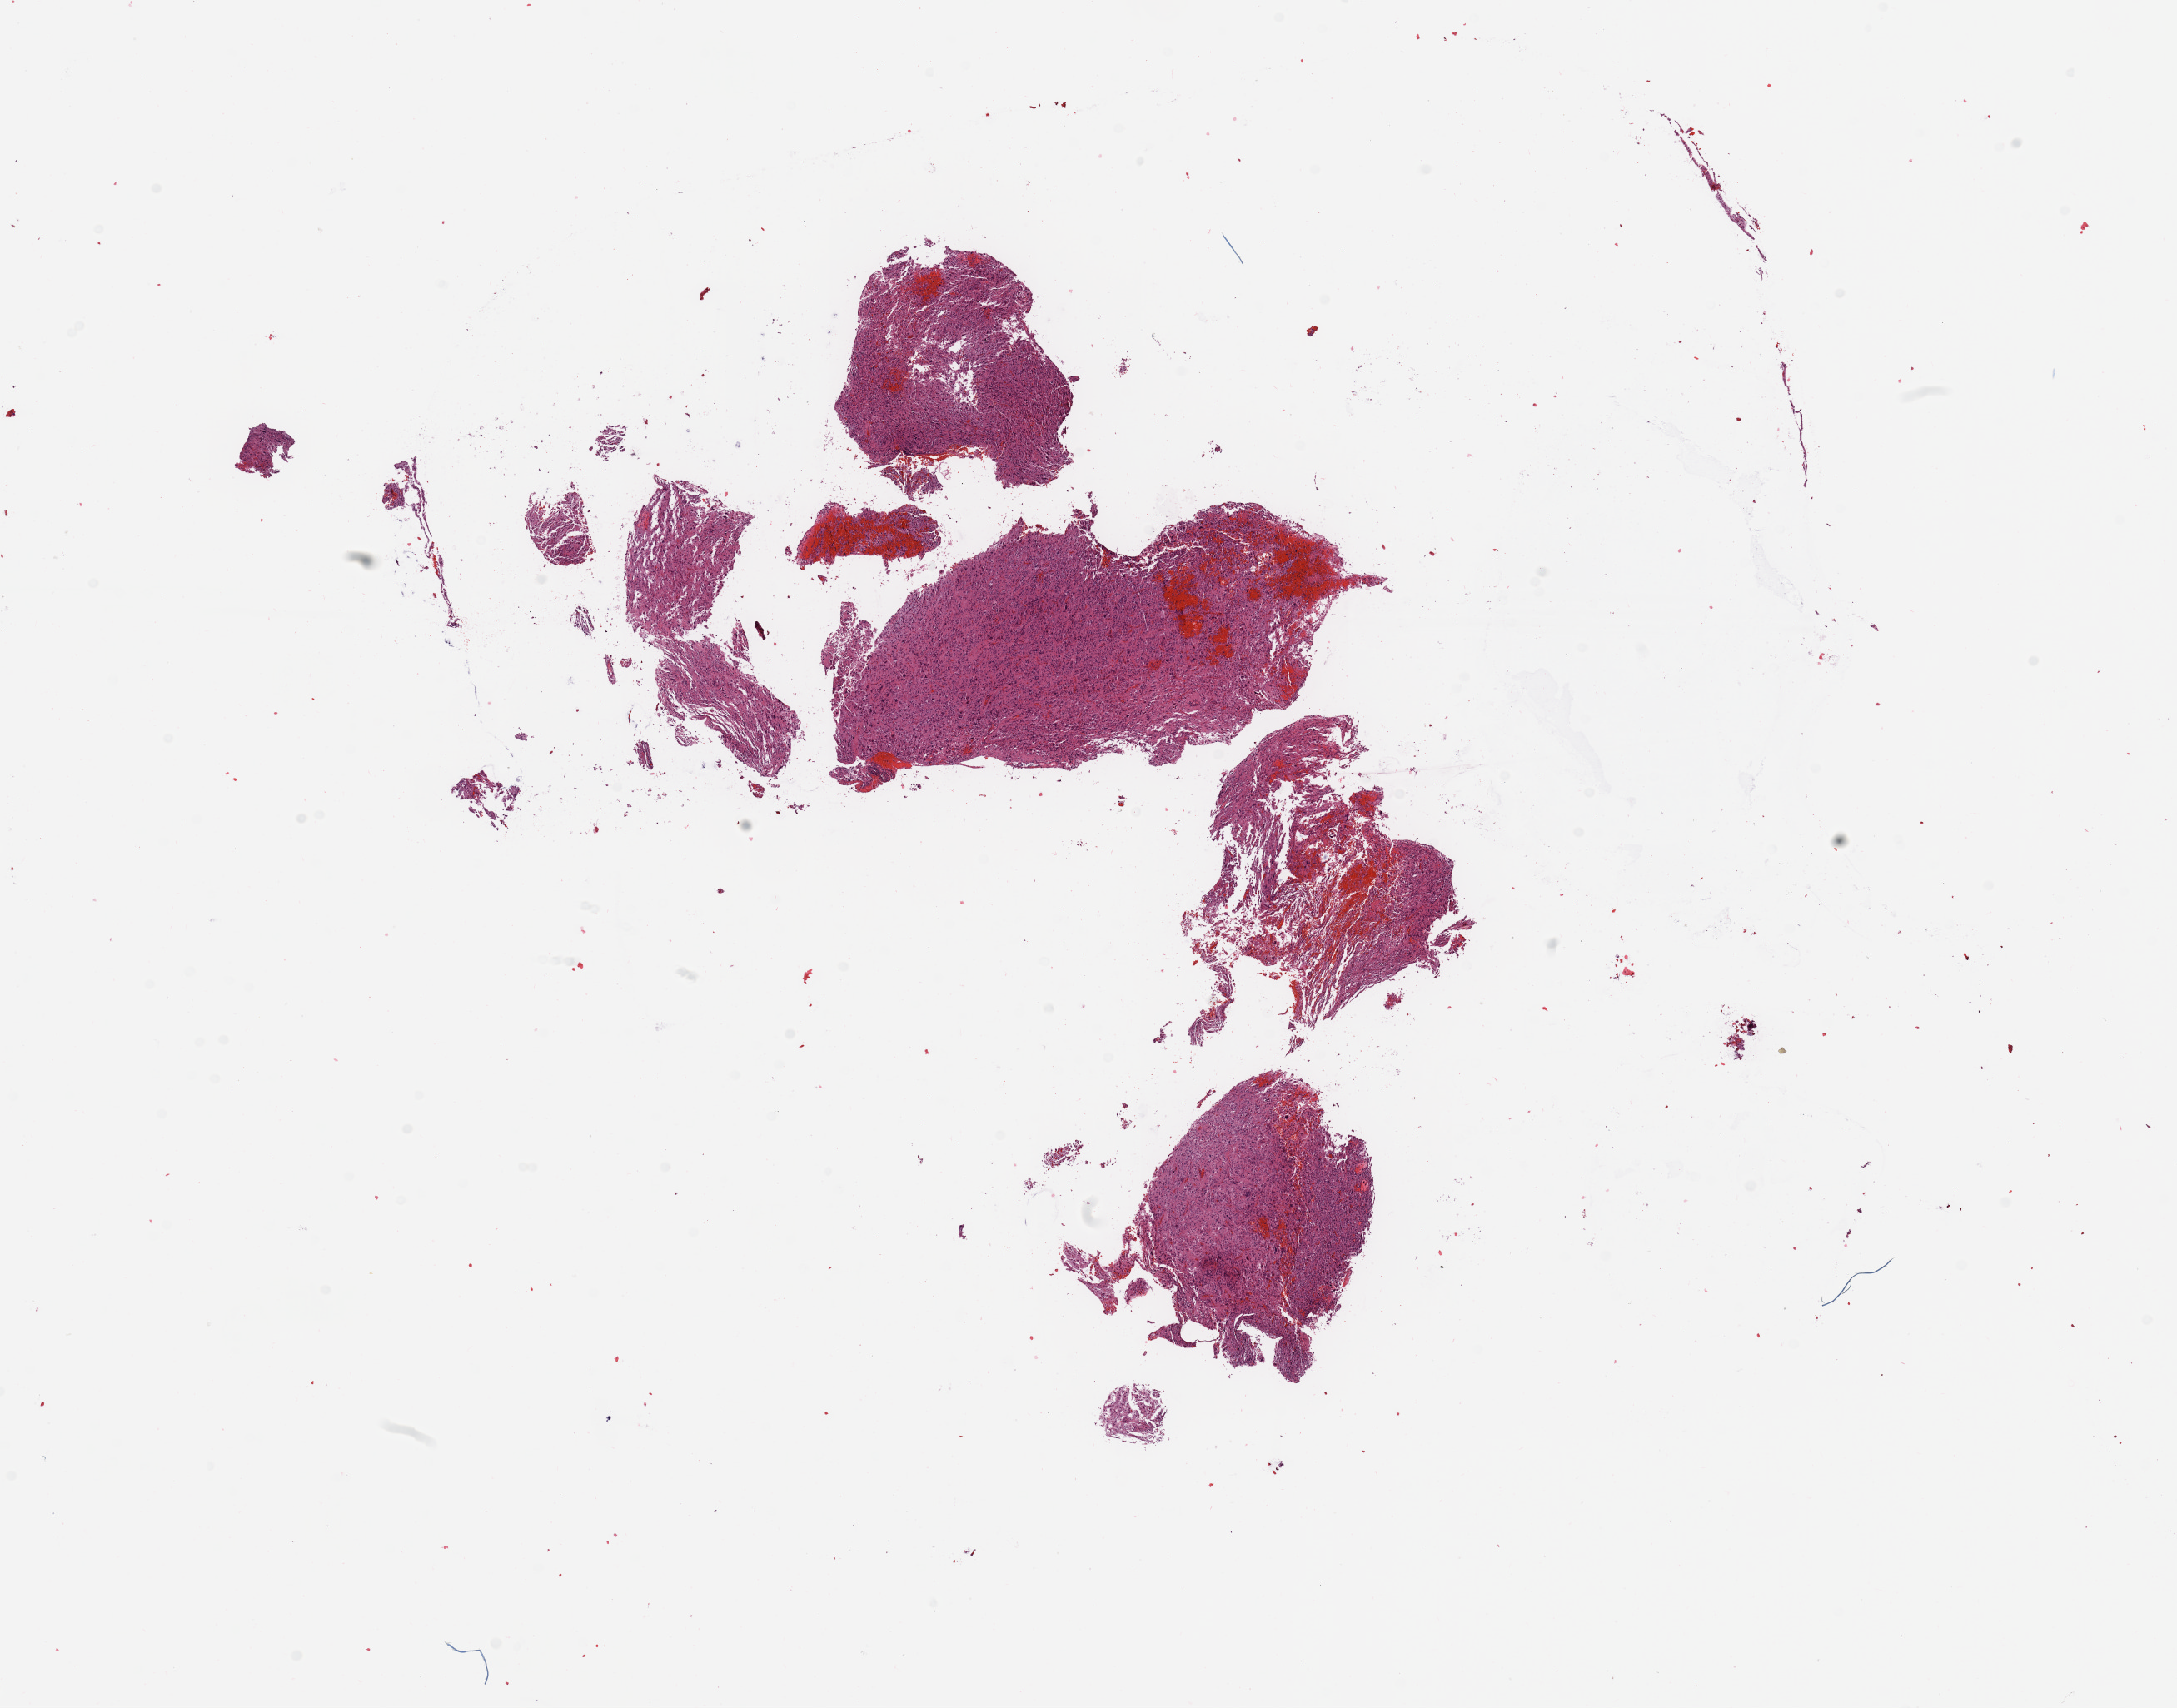
Whole-slide histology image, H&E — shown as a low-resolution overview of the whole scanned area (about 20.7 x 16.2 mm, from a 20x scan); tumour tissue sample, sampled site: frontal lobe. 50-year-old male patient. Composition of this section per pathologist review: tumour nuclei 85%, necrosis 2%.
- histologic diagnosis: Glioblastoma
- primary tumour site (as recorded): frontal lobe